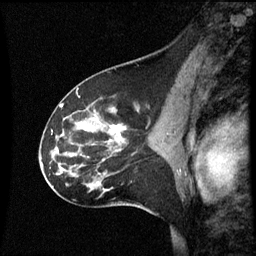
Breast MRI (dynamic contrast-enhanced), one sagittal slice. Slice 35 of 60 in the series (ordered by position). Dynamic contrast-enhanced series, image 2 of 3 at this slice position (ordered by acquisition). 1.5 T. TE 4.2 ms, TR 8.9 ms. 256 × 256 image matrix, field of view 200 × 200 mm. Female patient, age 45 years. From the clinical record (not read from this slice): setting: breast cancer imaged before/during neoadjuvant chemotherapy; receptor status: HR-positive, HER2-negative.
Outlined on this slice (semi-automatically segmented with operator editing):
- analysis volume of interest (the breast-tissue region the enhancement analysis was run in; not a lesion): bounding box [x1, y1, x2, y2] px = [46, 94, 171, 205]
- tumour enhancement mask (voxels above the 70 % enhancement threshold inside the analysis volume of interest): [110, 126, 127, 139]